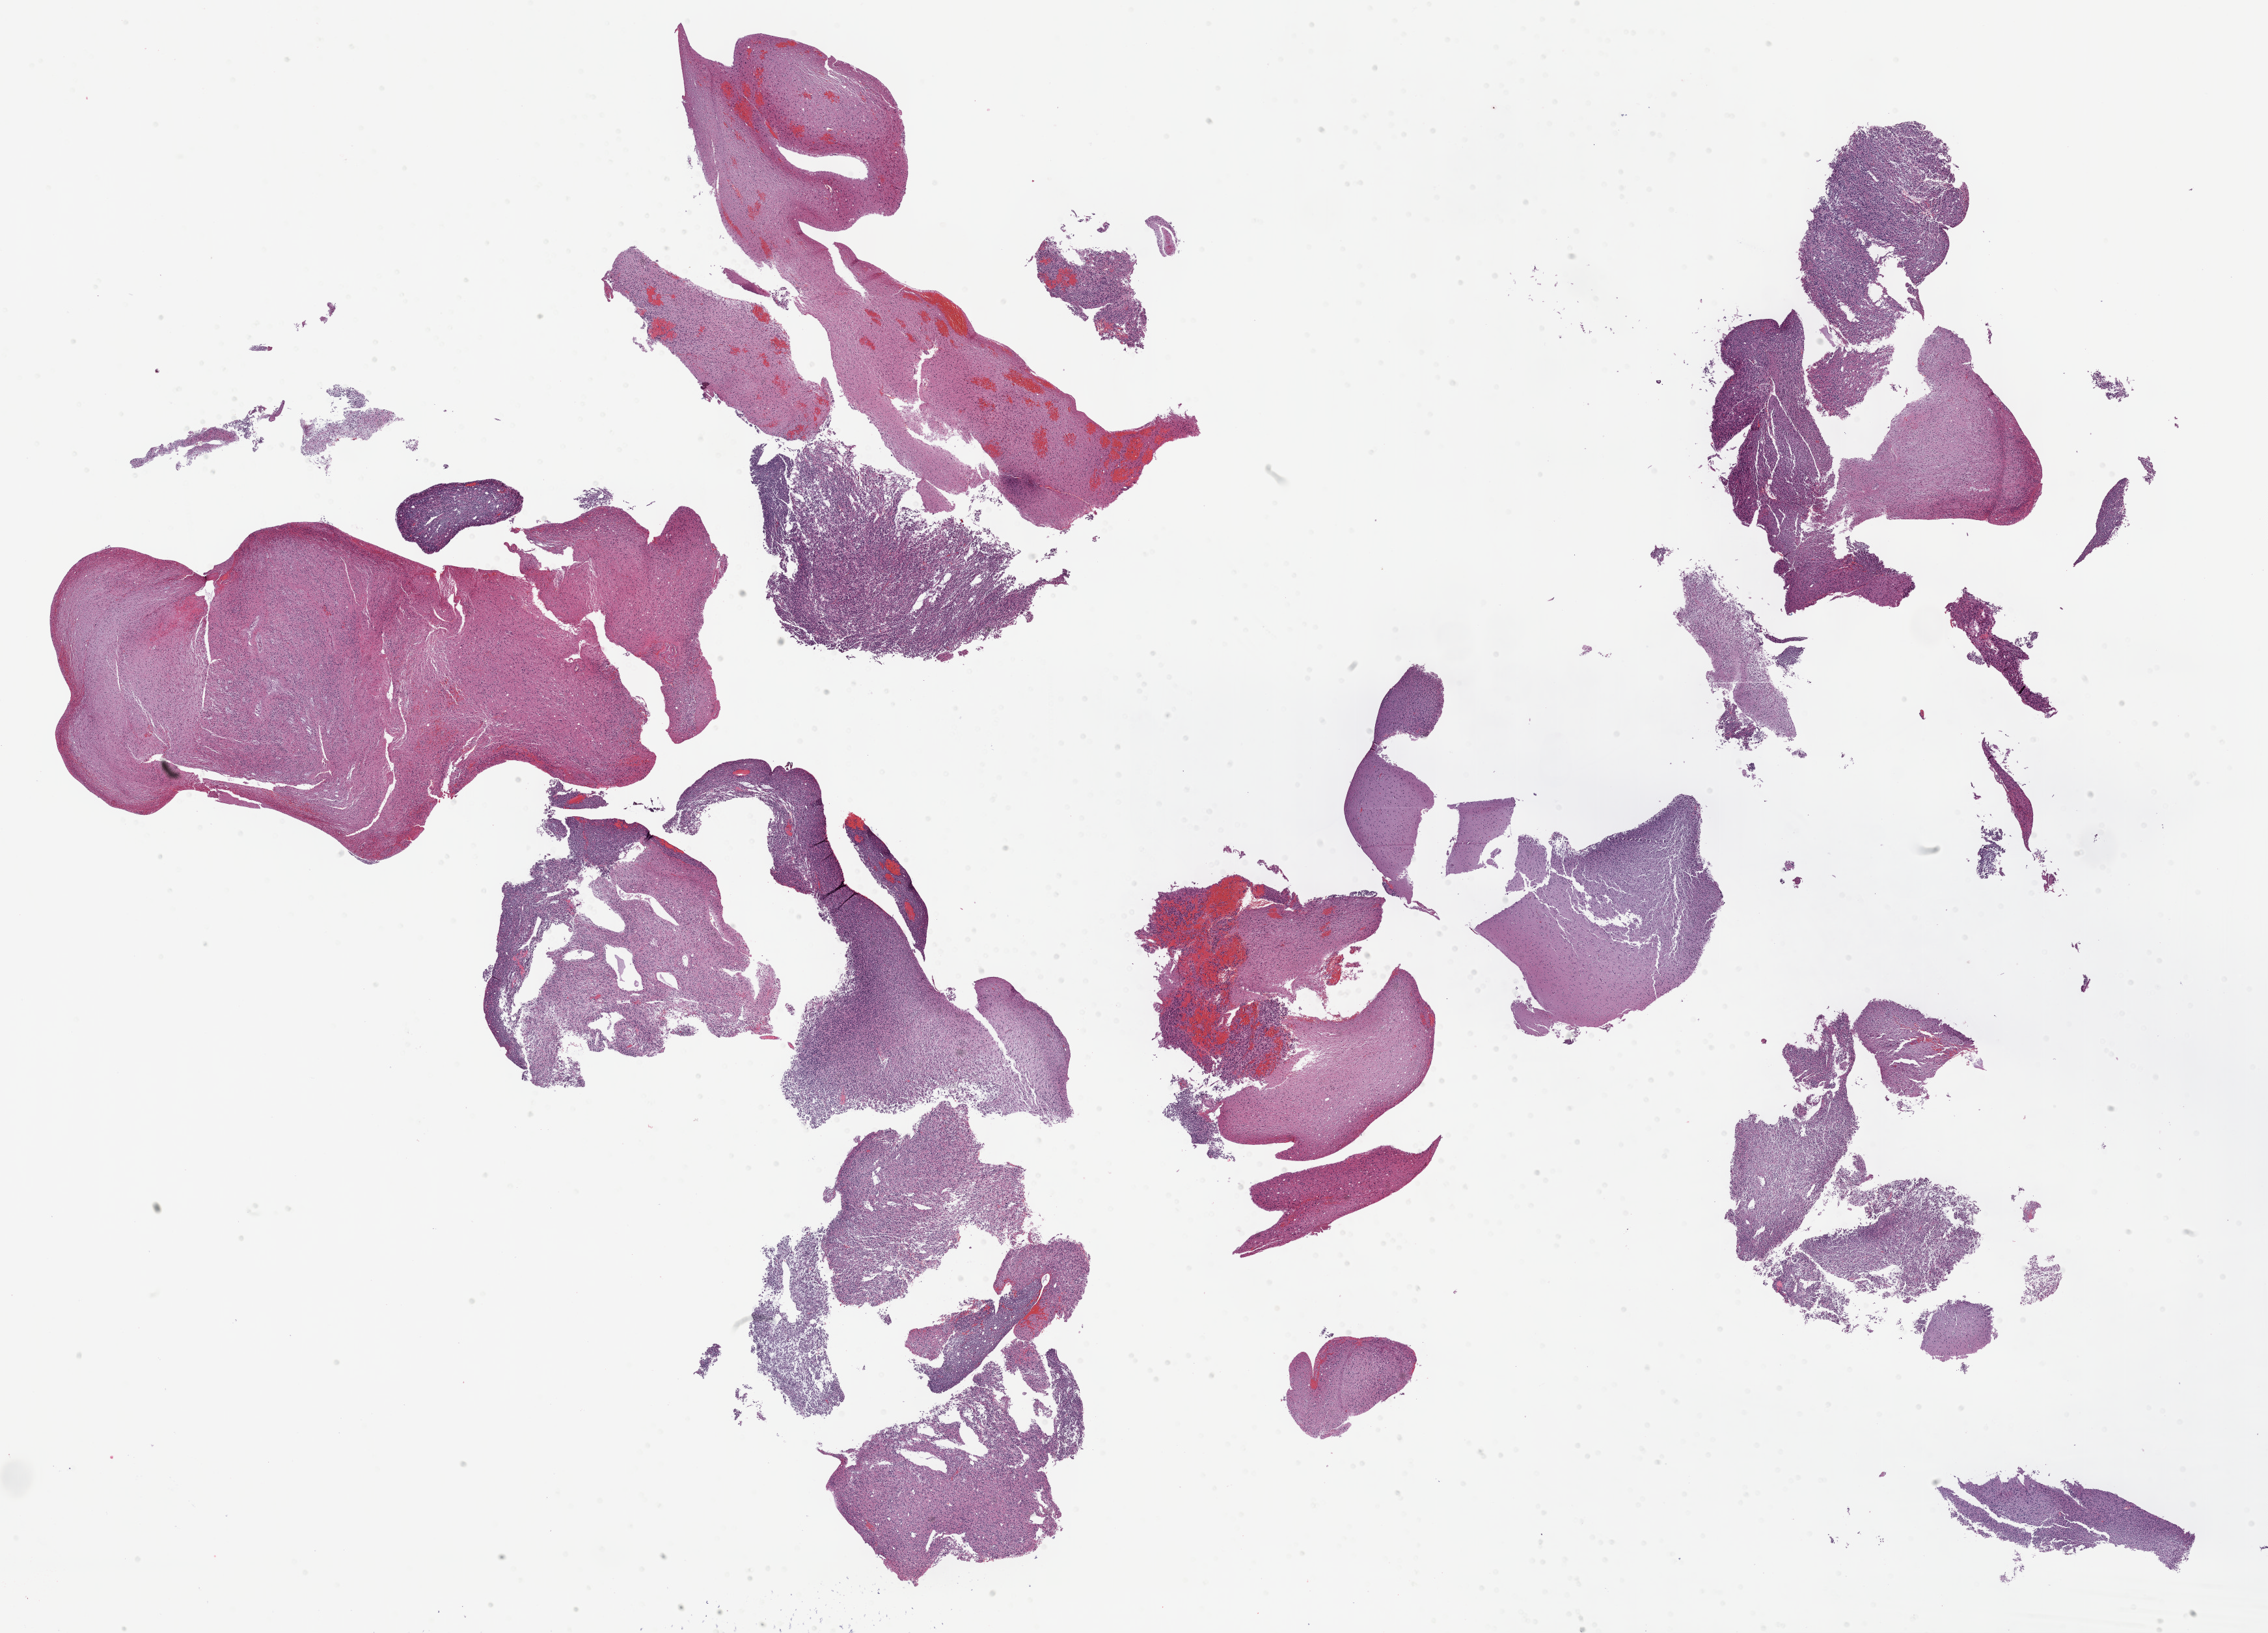
Whole-slide histology image, H&E, shown as a low-resolution overview of the whole scanned area (about 28.2 x 20.3 mm). Formalin-fixed paraffin-embedded (FFPE) diagnostic section. Primary tumour sample from the brain. Patient: female, age at initial diagnosis 44 years. Histologic grade: G3 (poorly differentiated).
Diagnosis: Astrocytoma, anaplastic (cerebrum). Laterality: left.